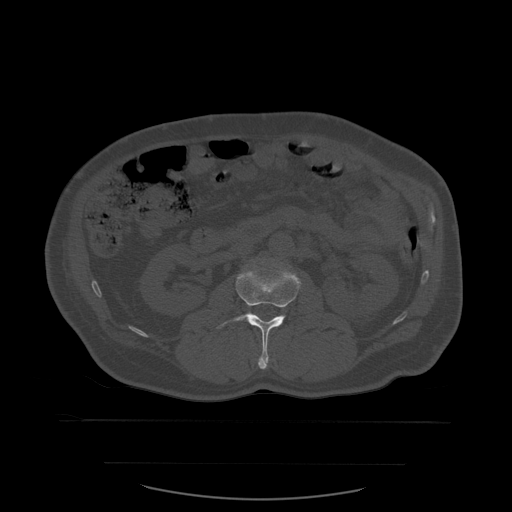
CT including the spine, one axial slice. Slice 216 of 590 in the series (ordered by position). Bone window (W 1800 / L 400 HU). 1.25 mm slice thickness. 512 × 512 image matrix, field of view 479 × 479 mm. Patient age 71 years. Case-level facts recorded for this patient, not image findings: primary cancer: lung.
Outlined on this slice (semi-automatically segmented with operator editing):
- L2 vertebra: bounding box (x1, y1, x2, y2) in pixels: (216, 266, 302, 370)